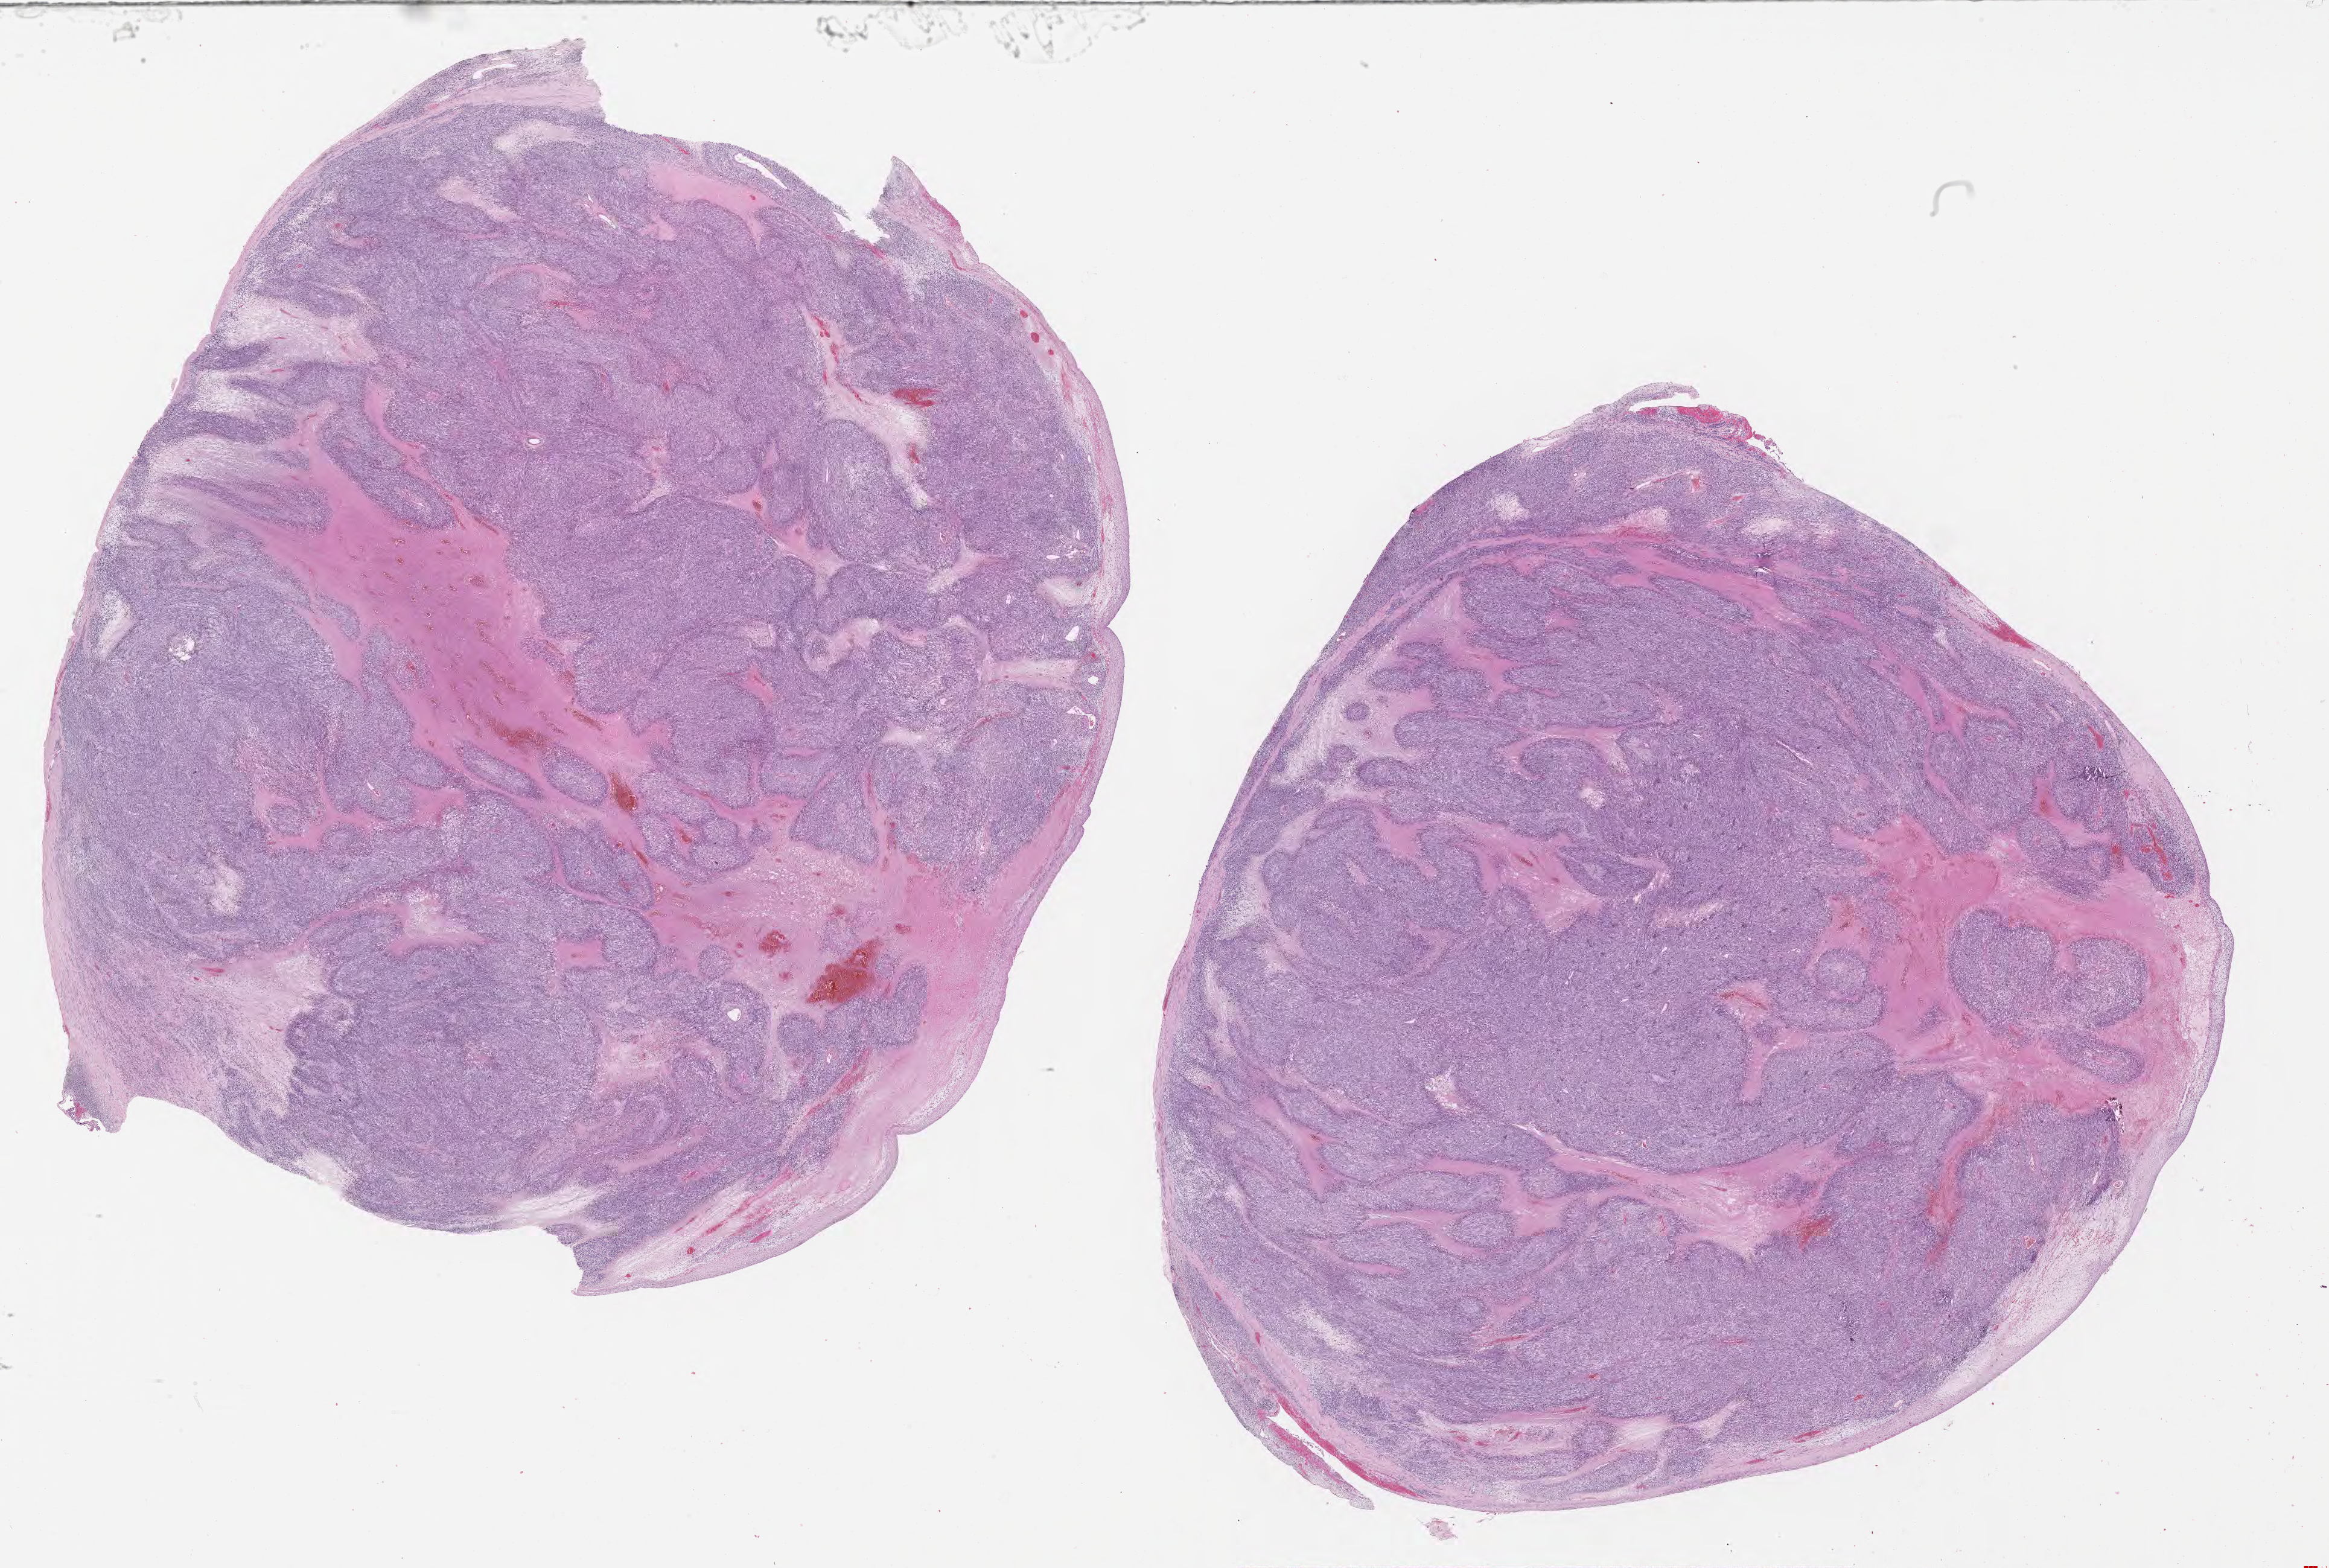
Digitized haematoxylin and eosin-stained section of tumor tissue — a low-resolution overview of the entire scanned area, about 31.2 x 21.0 mm; formalin-fixed paraffin-embedded section; site: soft tissue - testicle, right. Male patient, age at diagnosis 8.2 years.
Metastatic status at presentation (as recorded): non-metastatic. Stage (as recorded): 1. Diagnosis: rhabdomyosarcoma; histological classification: embryonal rhabdomyosarcoma.